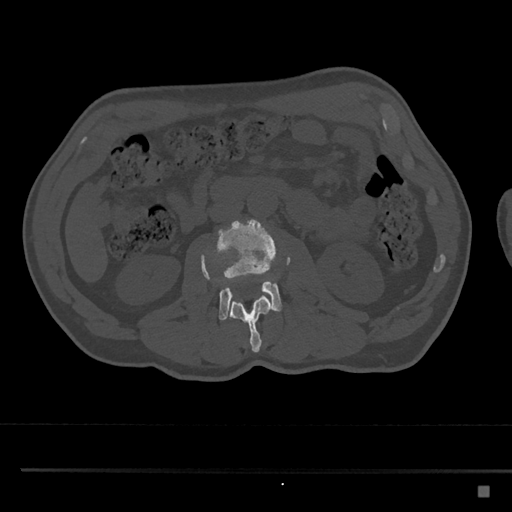
CT including the spine, one axial slice; slice 728 of 797 in the series (ordered by position); reconstruction kernel Br40s/3; 120 kVp; bone window (W 1800 / L 400 HU); 0.5 mm slice thickness; 512 × 512 image matrix, field of view 391 × 391 mm. Male patient, age 59 years. From the clinical record (not read from this slice): primary cancer: prostate.
Outlined on this slice (semi-automatic segmentation, software-assisted and operator-edited):
- L2 vertebra: bounding box (x1, y1, x2, y2) in pixels: (201, 255, 273, 352)
- L3 vertebra: (201, 219, 291, 320)